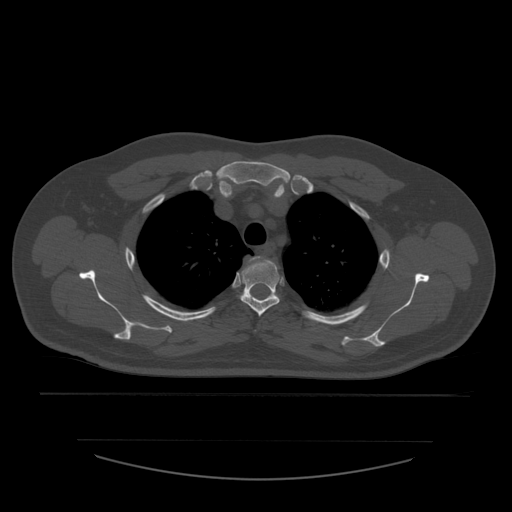
CT including the spine, one axial slice. Reconstruction kernel STANDARD. Bone window (W 1800 / L 400 HU). 1.25 mm slice thickness. 512 × 512 image matrix. Patient age 44 years. Case-level facts recorded for this patient, not image findings: primary cancer: soft tissue sarcoma.
Structures marked on this image (semi-automatically segmented with operator editing):
- T2 vertebra: bounding box [x1, y1, x2, y2] px = [250, 257, 262, 263]
- T3 vertebra: [241, 258, 280, 317]